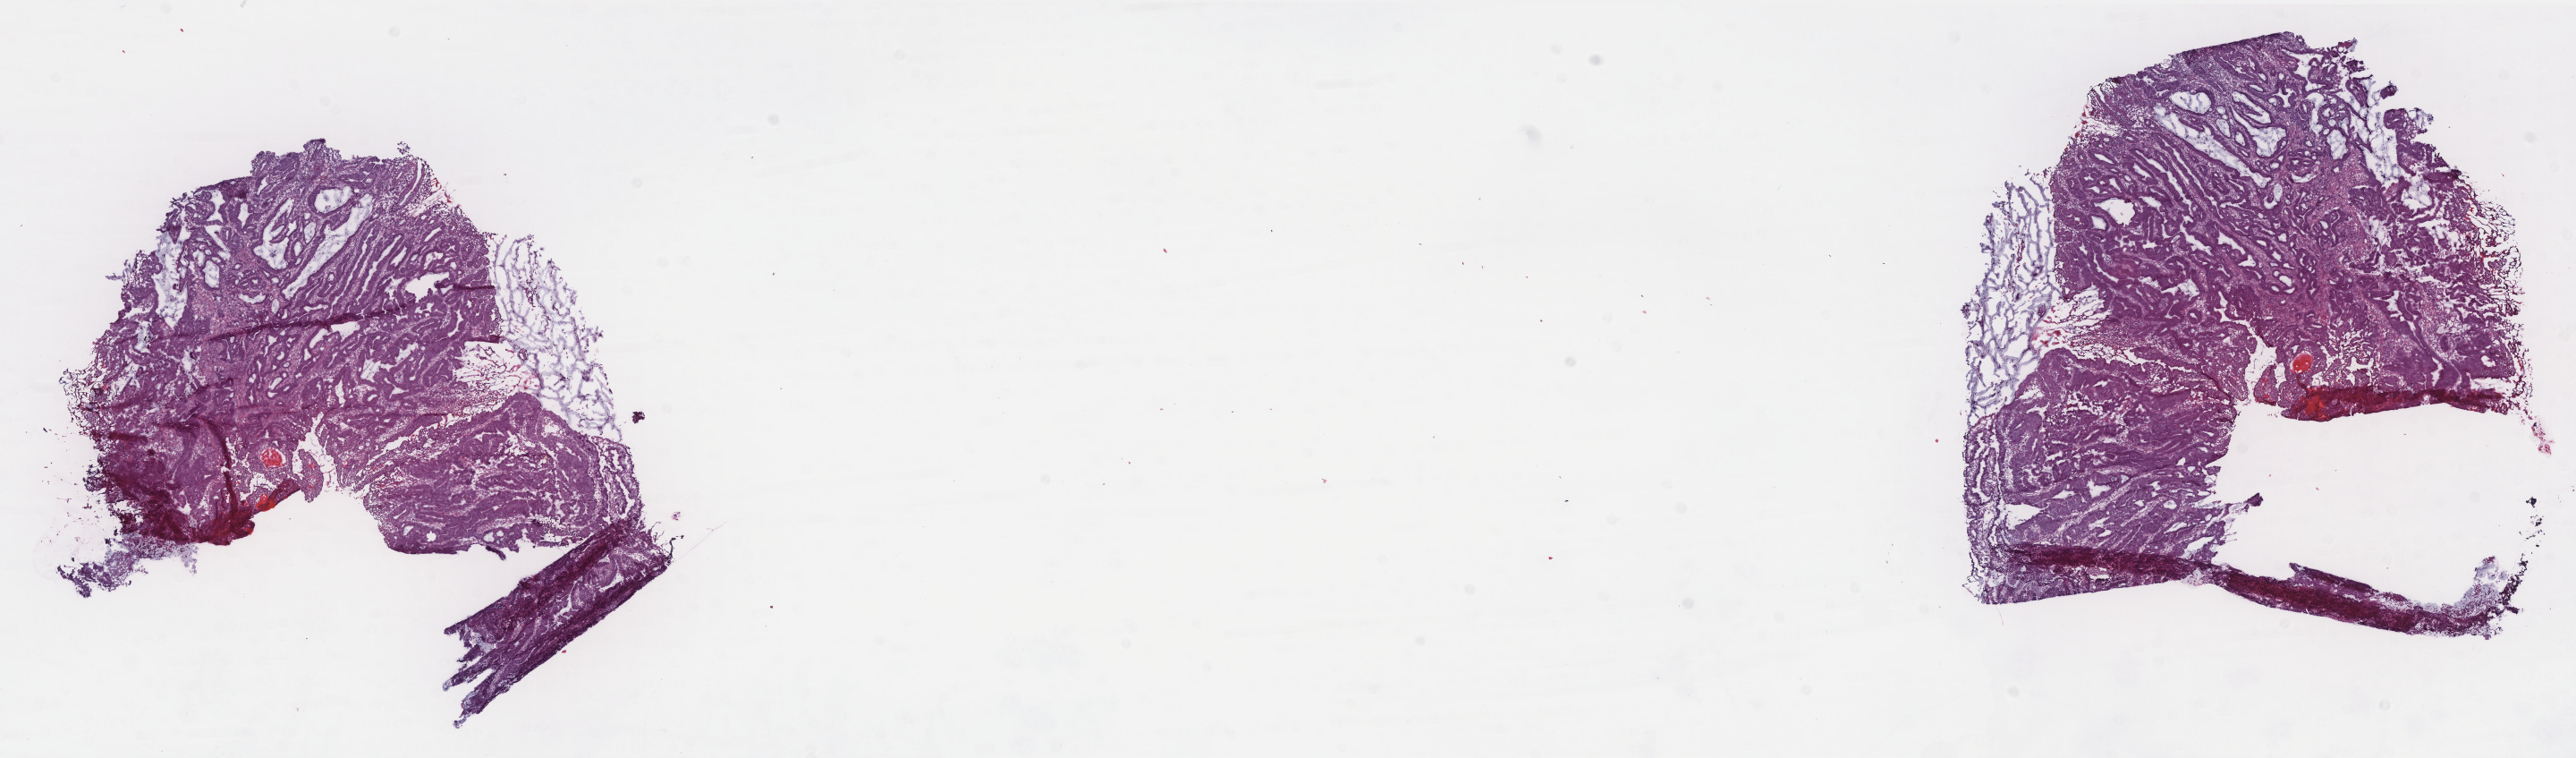
Whole-slide histology image, H&E — a low-resolution overview of the entire scanned area, about 23.1 x 6.8 mm (acquisition: 40x scan). Frozen section. Rectum, primary tumour sample. Patient: male, age at initial diagnosis 67 years. Slide review estimates, as recorded: tumour cells 85%, tumour nuclei 80%, normal cells 0%, stromal cells 13%, necrosis 2%. Inflammatory infiltration, as recorded: lymphocyte infiltration 8%, monocyte infiltration 2%, neutrophil infiltration 2%.
AJCC pathologic stage: II (5th edition). Diagnosis: Adenocarcinoma, NOS. Lymph nodes positive (case pathology): 0 of 12 examined.